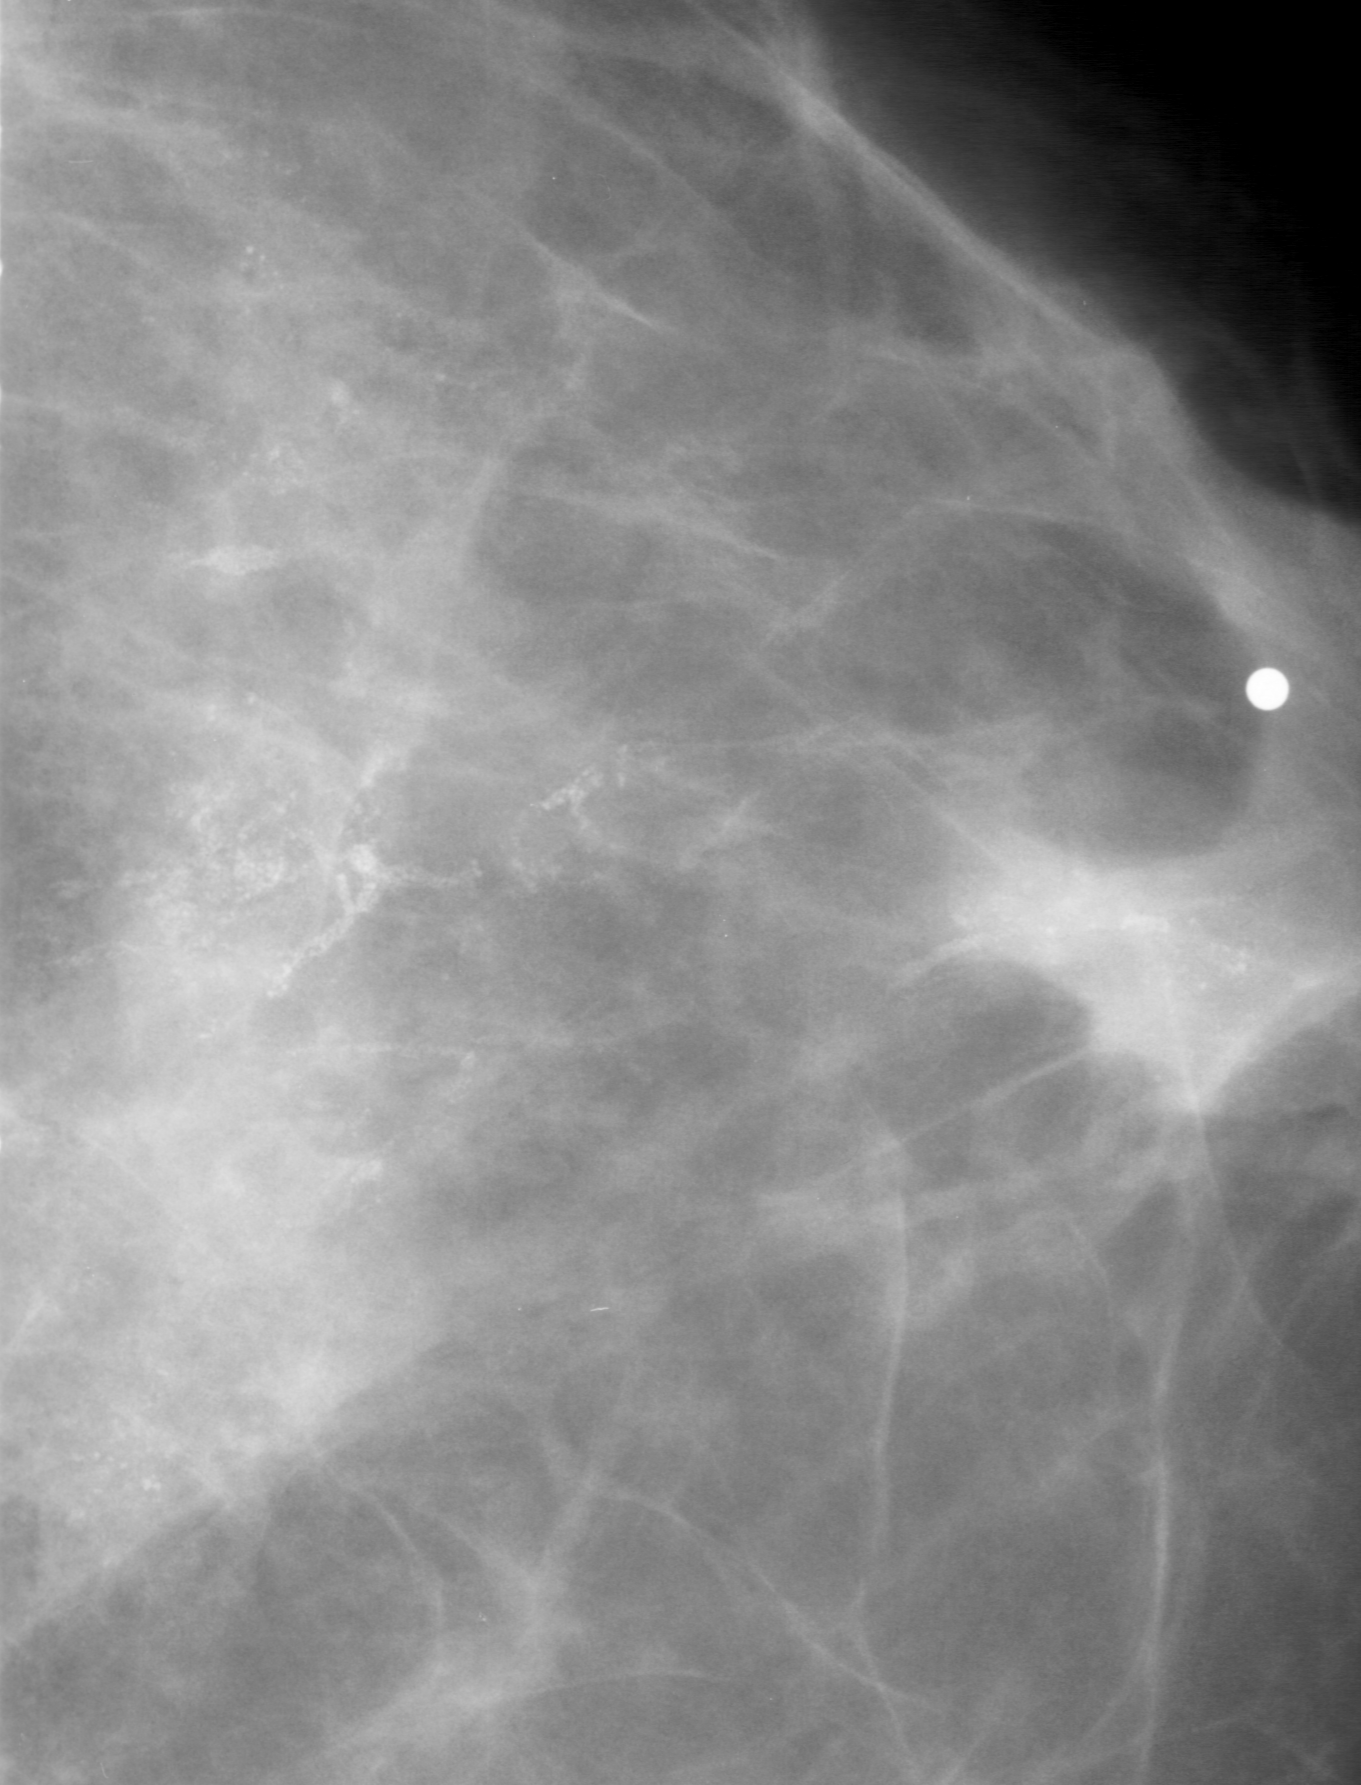
Crop from a digitized film mammogram around one marked abnormality, left breast, CC view, BI-RADS breast density category 2 (scale 1–4).
- Calcifications, morphology amorphous, distribution linear; BI-RADS assessment category 5; subtlety rating 5 on a 1 (subtle) to 5 (obvious) scale; pathology (as recorded): malignant.